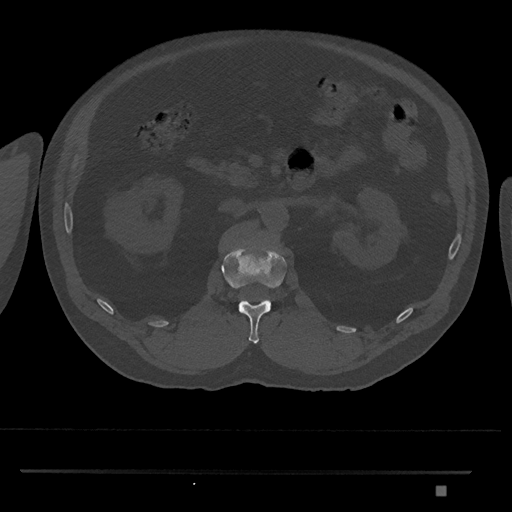
CT including the spine, one axial slice; slice 806 of 1134 in the series (ordered by position); reconstruction kernel Br40s/3; 120 kVp; bone window (W 1800 / L 400 HU); 512 × 512 image matrix. Patient: male, 65 years. From the clinical record (not read from this slice): primary cancer: prostate.
Structures marked on this image (semi-automatically segmented with operator editing):
- L1 vertebra: bounding box <221,246,287,344> (left, top, right, bottom; pixels)